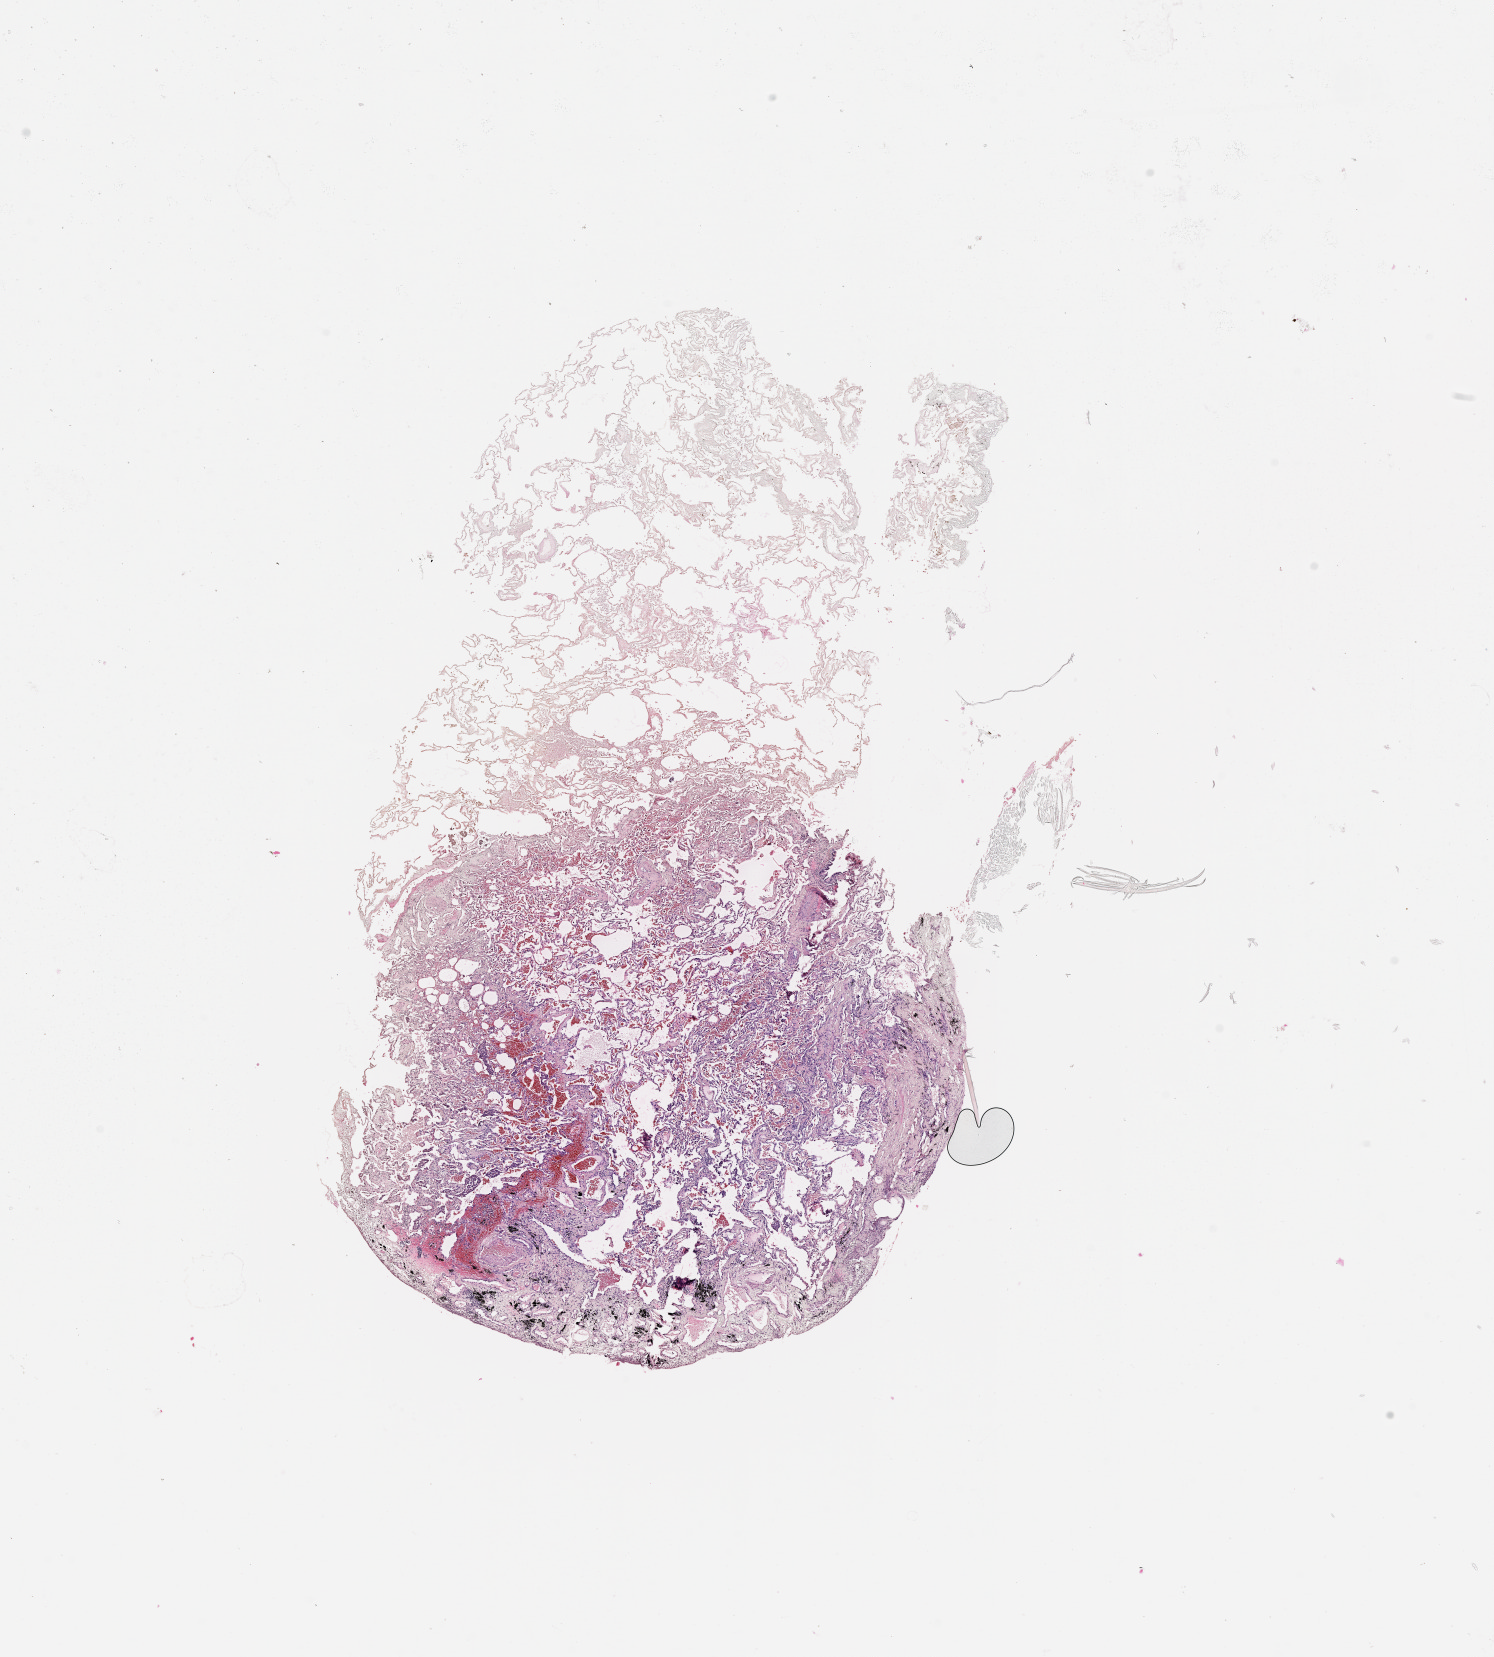
H&E whole-slide image, low-resolution overview of the scanned area, about 12.0 x 13.3 mm (acquisition: 20x scan), normal (non-tumour) tissue sample, lung. Patient: male, age 68 years.
This section: normal (non-tumour) tissue from the same patient. Patient diagnosis: Adenocarcinoma, NOS.